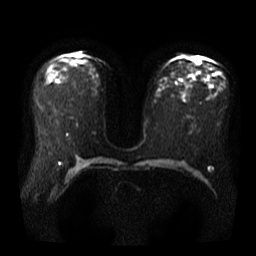
Breast MRI, one axial slice; position 22 of 40 along the scan axis; diffusion-weighted series; image 2 of 4 stored at this slice position (different b-values; order by instance number); 3 T; 256 × 256 image matrix, field of view 360 × 360 mm. Female patient.
Outlined on this slice (expert manual segmentation):
- tumour on diffusion-weighted imaging: box from (x=187, y=55) to (x=192, y=60) px